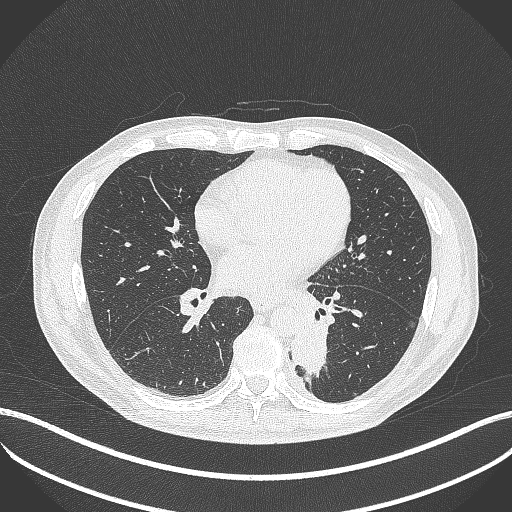
Chest CT, one axial slice. Slice 183 of 451 in the series (ordered by position). Lung window (W 1500 / L -600 HU). 1 mm slice thickness. 512 × 512 image matrix, field of view 400 × 400 mm. Male patient, age 72 years. Case-level facts recorded for this patient, not image findings: clinical TNM (as recorded): T2b N0 M1.
Structures marked on this image (rectangle marked by the reading radiologist):
- lung tumour (recorded histology: adenocarcinoma): box from (x=290, y=318) to (x=333, y=378) px